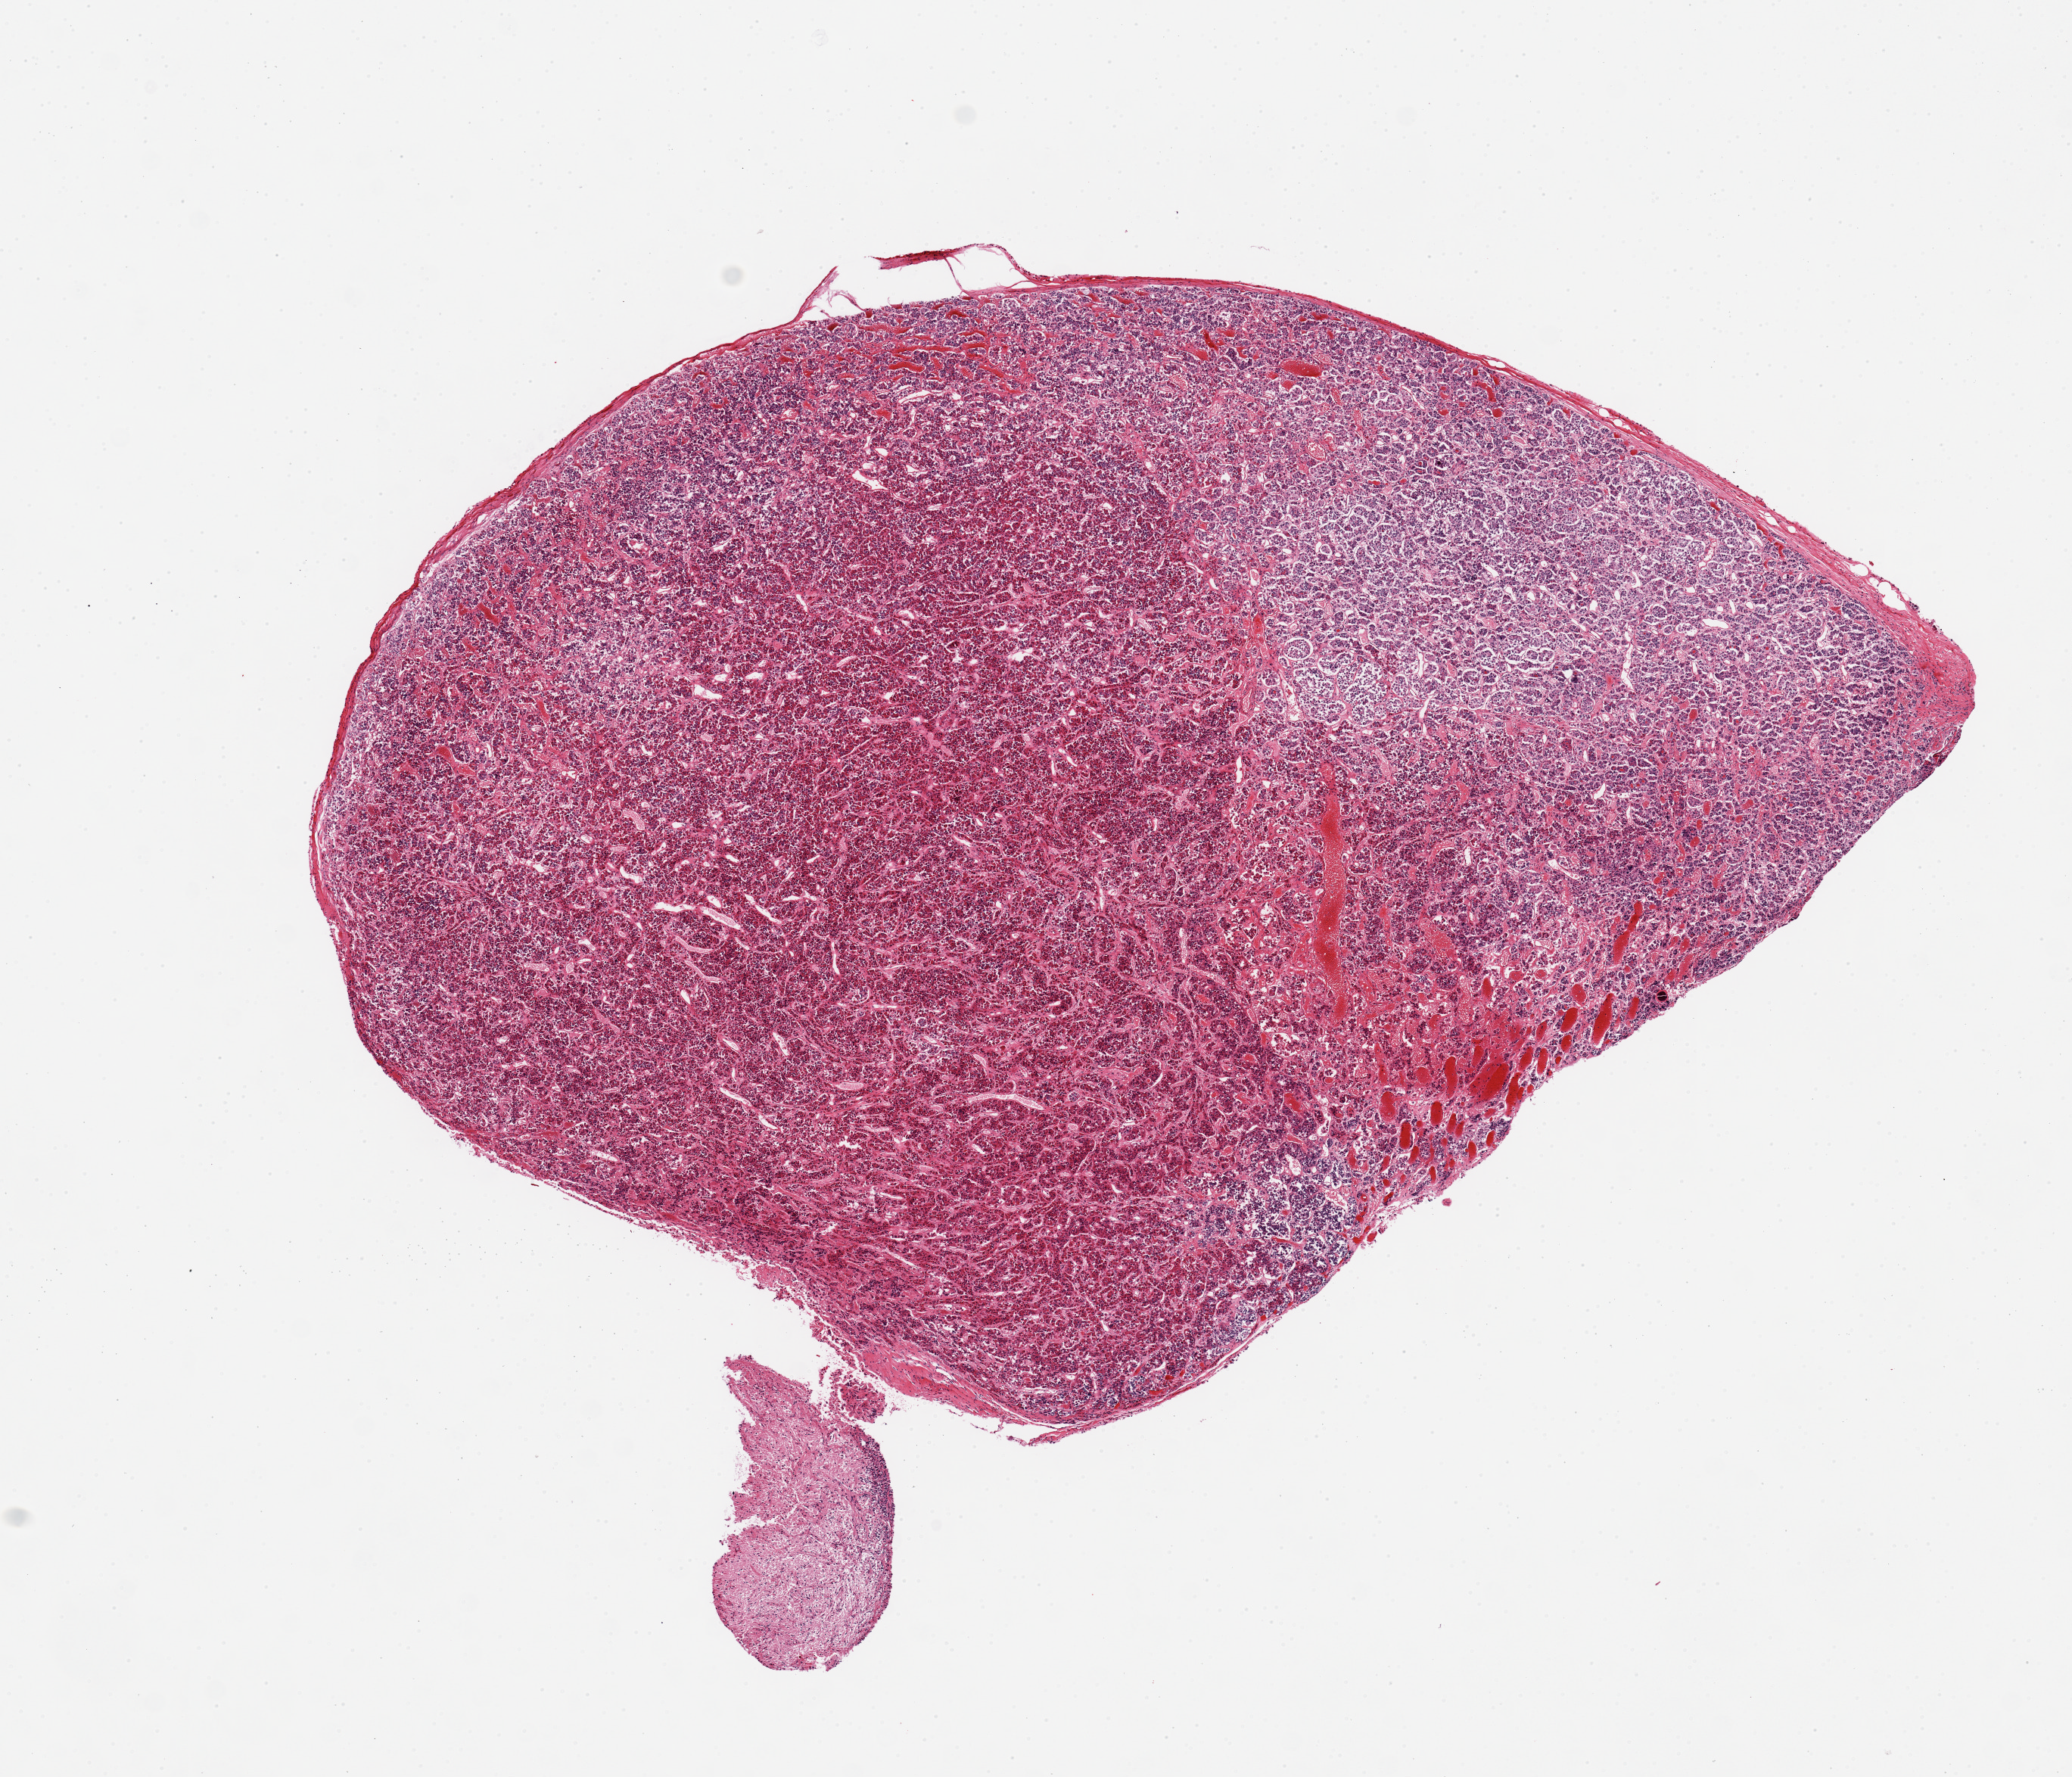
Whole-slide image, H&E stain, brightfield — low-resolution overview of the scanned area, about 10.8 x 9.3 mm; PAXgene-fixed, paraffin-embedded tissue; sampled site (target tissue): pituitary; tissue donor sample. Donor sex: male.
* pathologist's review note for this sample: 2 pieces, predominantly adenohypophysis, small detached fragment of neurohypophysis